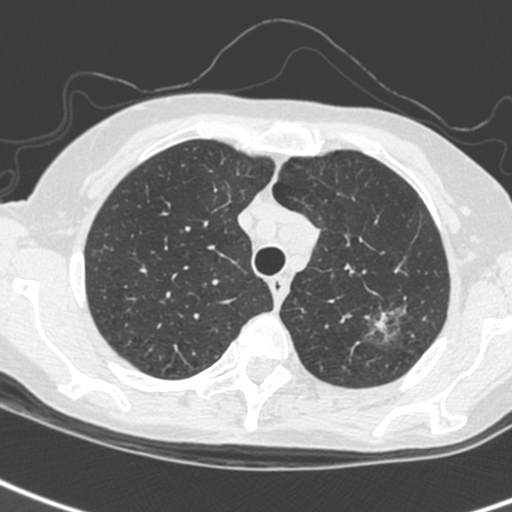
Chest CT (low-dose screening protocol), one axial image. Baseline screening round. Lung window (W 1500 / L -600 HU). 1.3 mm slice thickness. 120 kVp. Female participant, aged 61 years at enrolment.
Lesion marked by an expert reader, box from (x=352, y=303) to (x=412, y=351) px. The screening reader recorded 2 non-calcified nodules or masses ≥4 mm on this exam (left upper lobe, left upper lobe); which of them this box marks is not recorded. Lung cancer was diagnosed 29 days after this screen: small cell carcinoma, NOS, left upper lobe, stage IV (AJCC 6th edition).